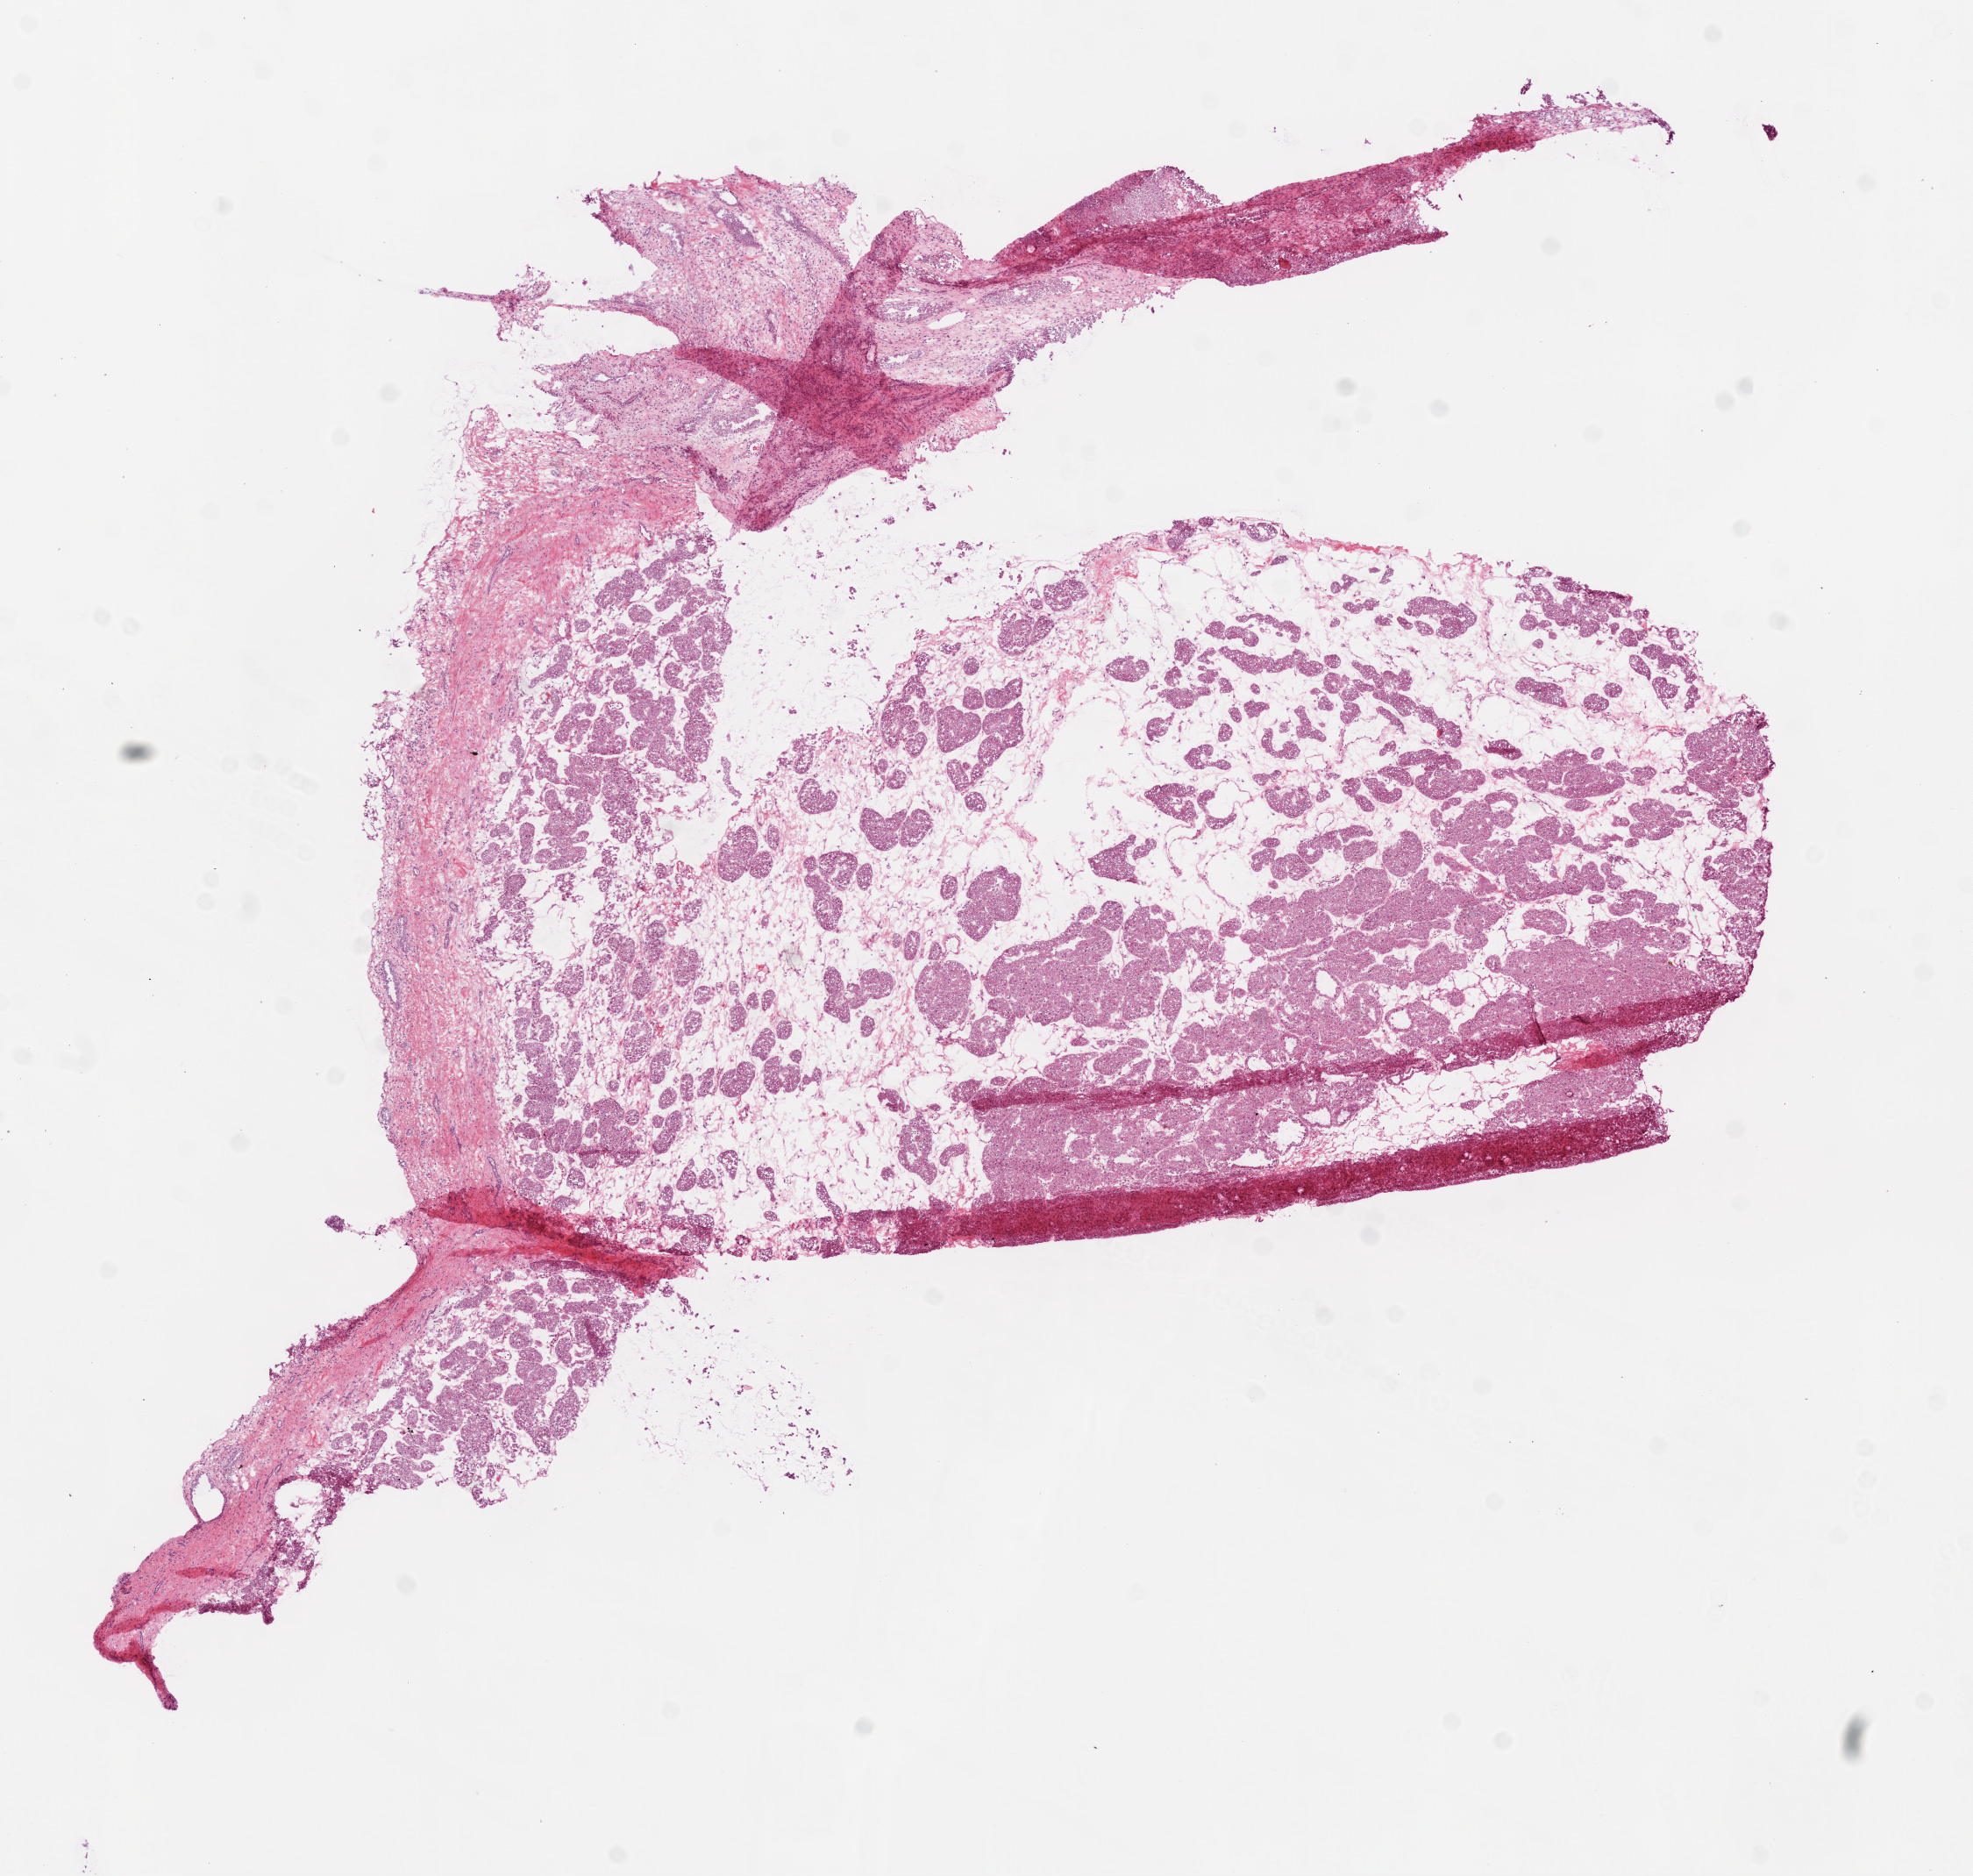
Whole-slide histology image, H&E-stained — shown as a low-resolution overview of the whole scanned area (about 9.0 x 8.6 mm, slide scanned at 20x); frozen section from the top of the tissue portion; sample: primary tumour, kidney. Patient: male, age at initial diagnosis 58 years. Histologic grade: G2 (moderately differentiated). Composition of this section per pathologist review: tumour cells 77%, tumour nuclei 80%, normal cells 3%, stromal cells 20%, necrosis 0%.
Laterality: left. AJCC pathologic stage: I (7th edition). Diagnosis: Clear cell adenocarcinoma, NOS. TNM: T1a N0 M0.